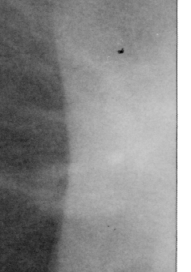
Cropped region of a digitized screen-film mammogram centred on a radiologist-marked abnormality; right breast; CC view.
Marked abnormality: mass, shape irregular, margins spiculated; BI-RADS assessment category 4; pathology (as recorded): malignant.